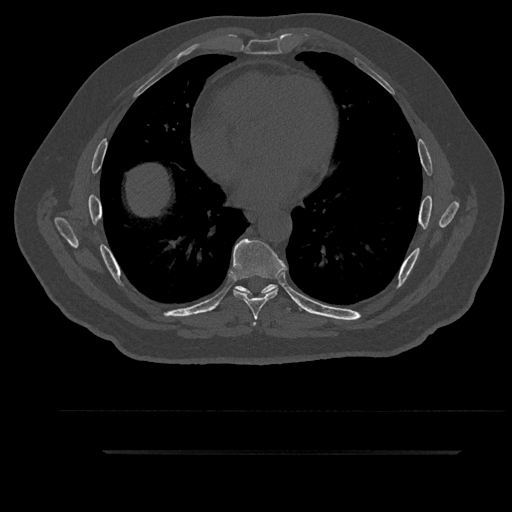
CT including the spine, one axial slice. Position 511 of 797 along the scan axis. Reconstruction kernel Br40s/3. 120 kVp. Bone window (W 1800 / L 400 HU). 512 × 512 image matrix, field of view 432 × 432 mm. Male patient, age 63 years. Case-level facts recorded for this patient, not image findings: primary cancer: renal; vertebrae with lytic lesions (as recorded): T8.
Outlined on this slice (semi-automatically segmented with operator editing):
- T6 vertebra: bounding box <235,288,270,325> (left, top, right, bottom; pixels)
- T7 vertebra: <231,238,287,320>
- T8 vertebra: <235,284,278,294>